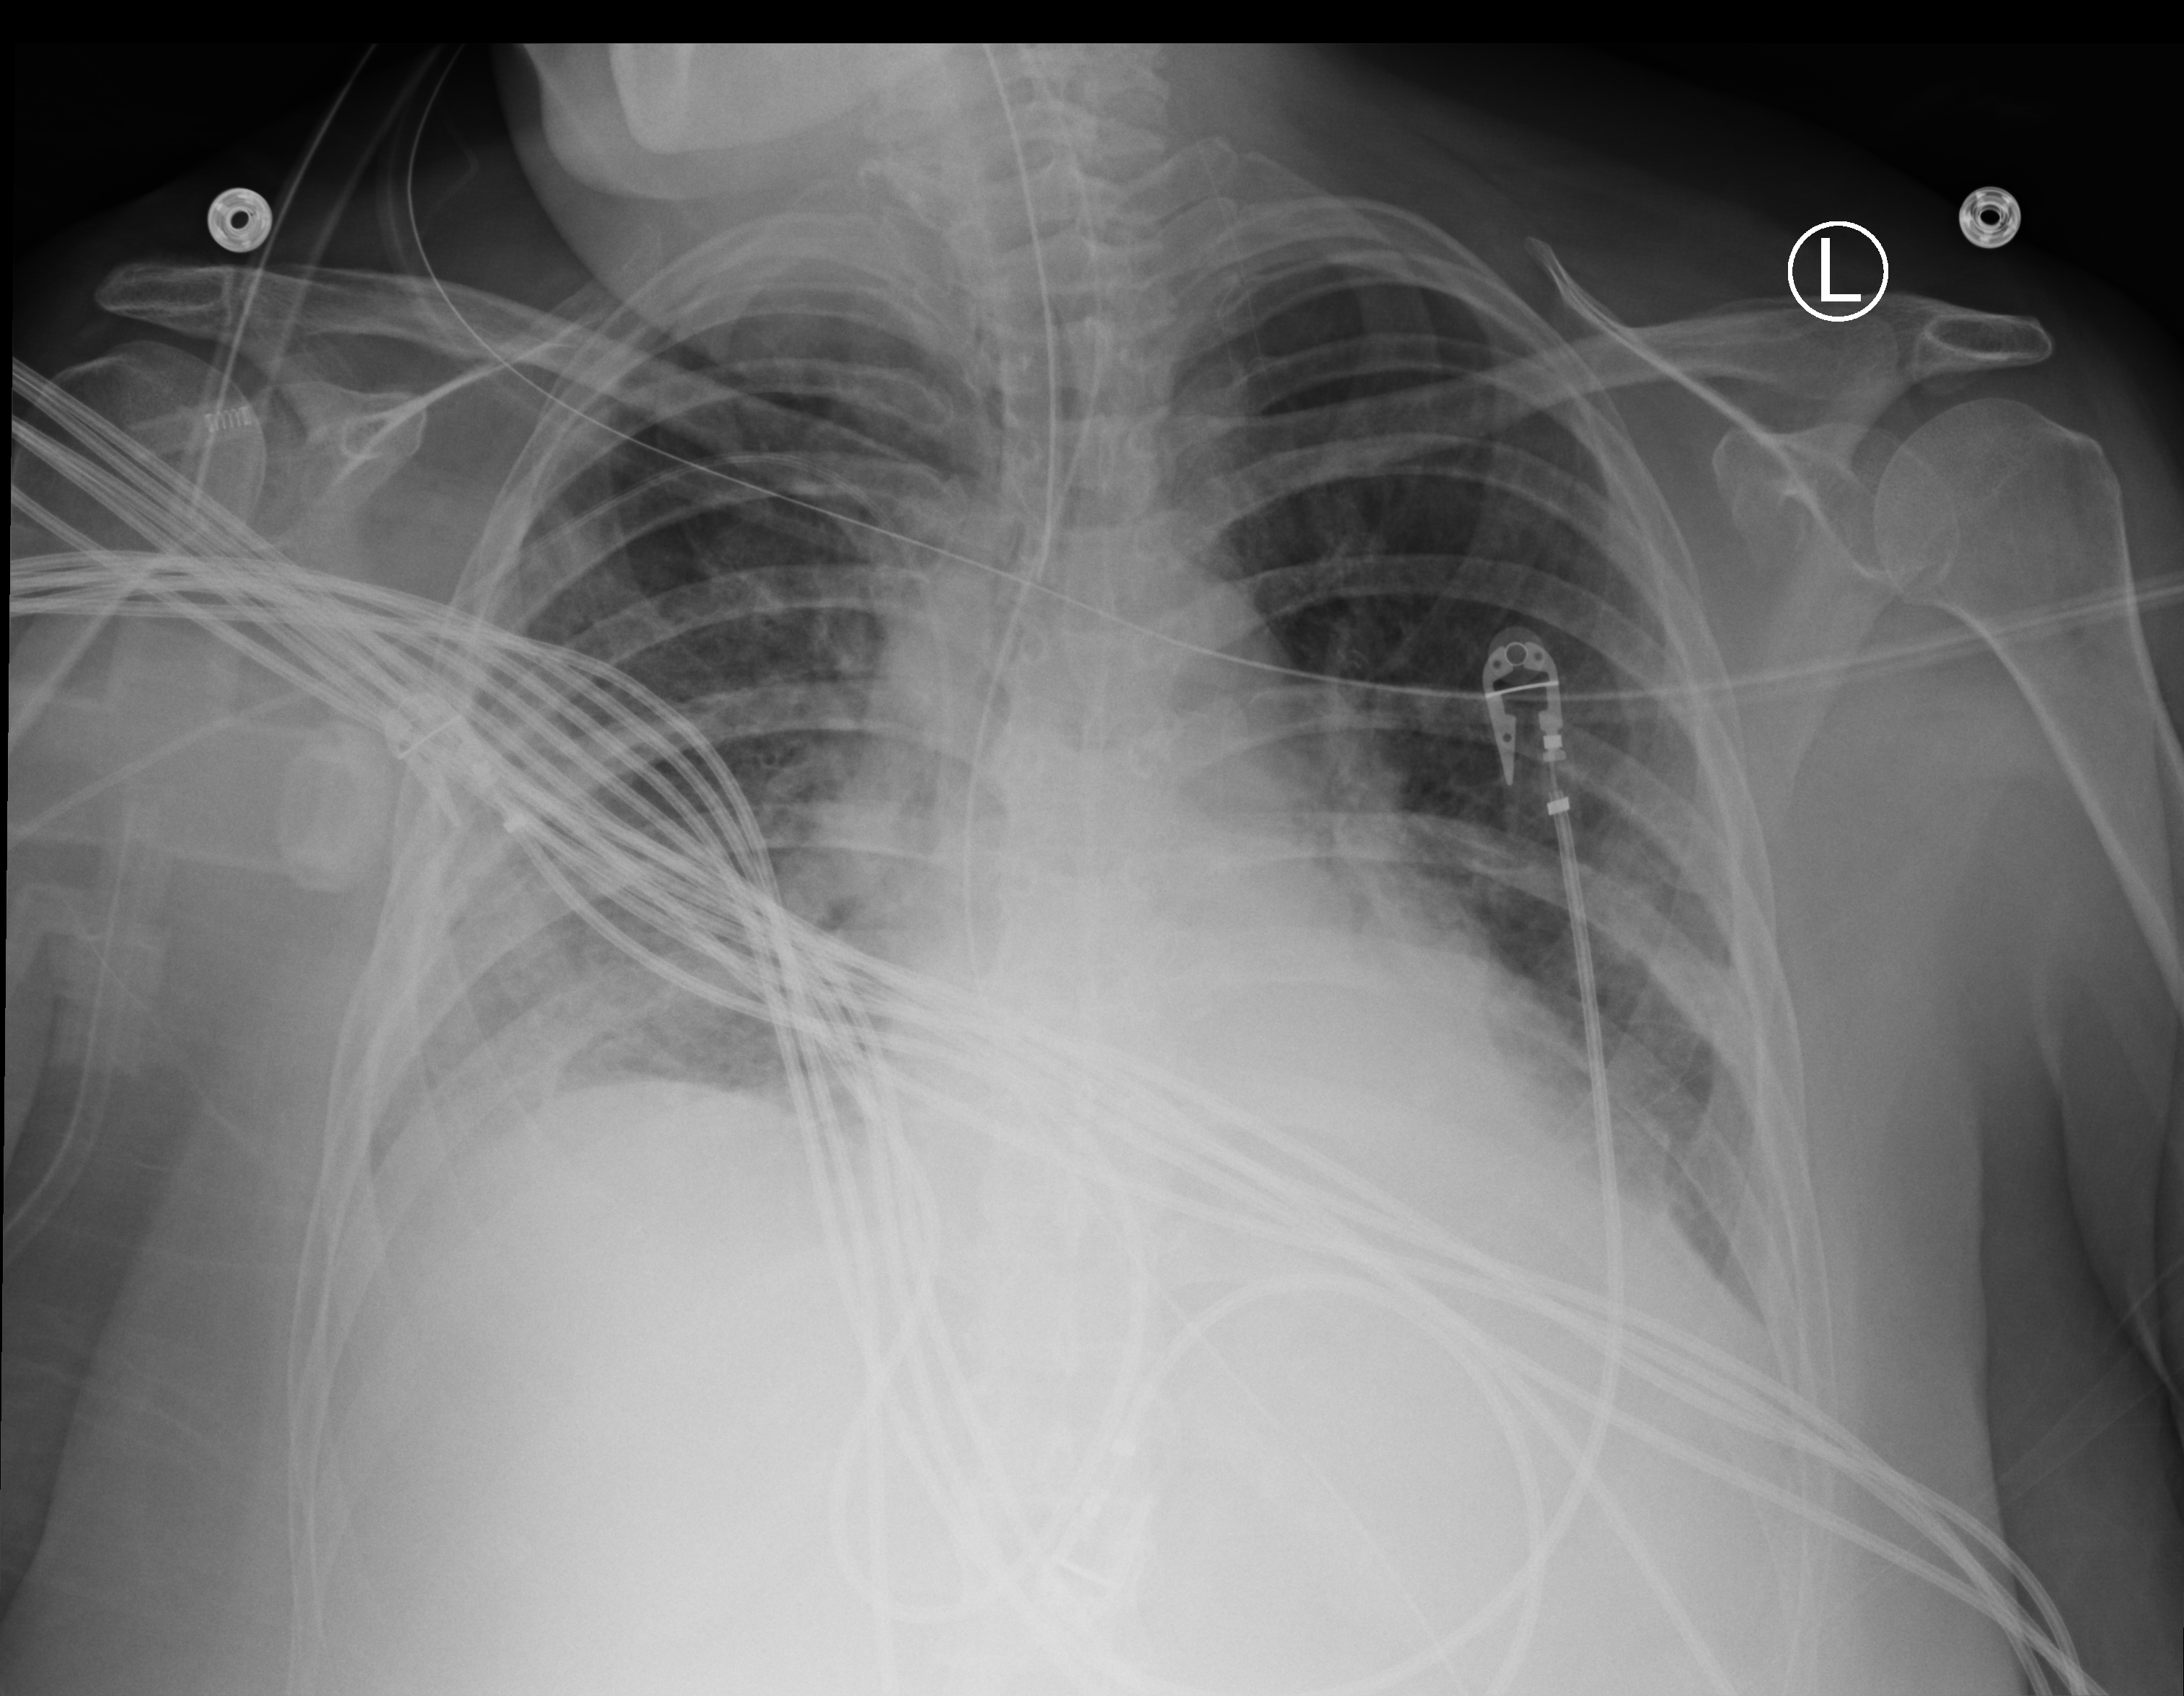
Chest X-ray (portable); anteroposterior (AP) projection. Female patient hospitalised with COVID-19, age 60–74 years.
Admission-level facts for this patient (not findings on this image; timing relative to this image not recorded): admitted to intensive care during this hospital stay: yes; length of hospital stay: 9 days.